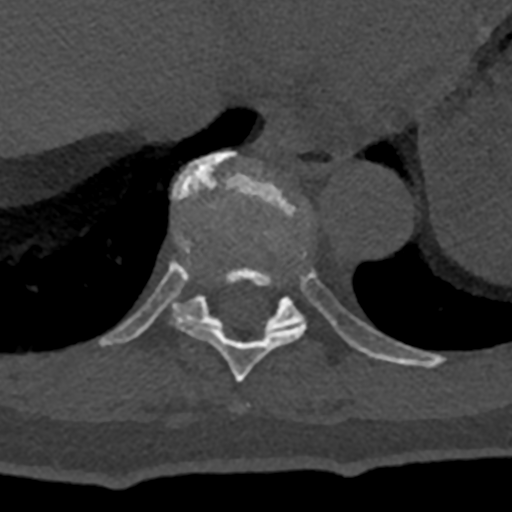
CT including the spine, one axial slice; slice 634 of 797 in the series (ordered by position); reconstruction kernel Br40s/3; 120 kVp; bone window (W 1800 / L 400 HU); 0.5 mm slice thickness; 512 × 512 image matrix, field of view 160 × 160 mm. Patient: male, 74 years. From the clinical record (not read from this slice): primary cancer: renal; vertebrae with lytic lesions (as recorded): T10, L1, L2, L3, L4, L5.
Structures marked on this image (semi-automatically segmented with operator editing):
- T10 vertebra: bounding box [x1, y1, x2, y2] px = [99, 151, 432, 368]
- T9 vertebra: [171, 249, 306, 383]